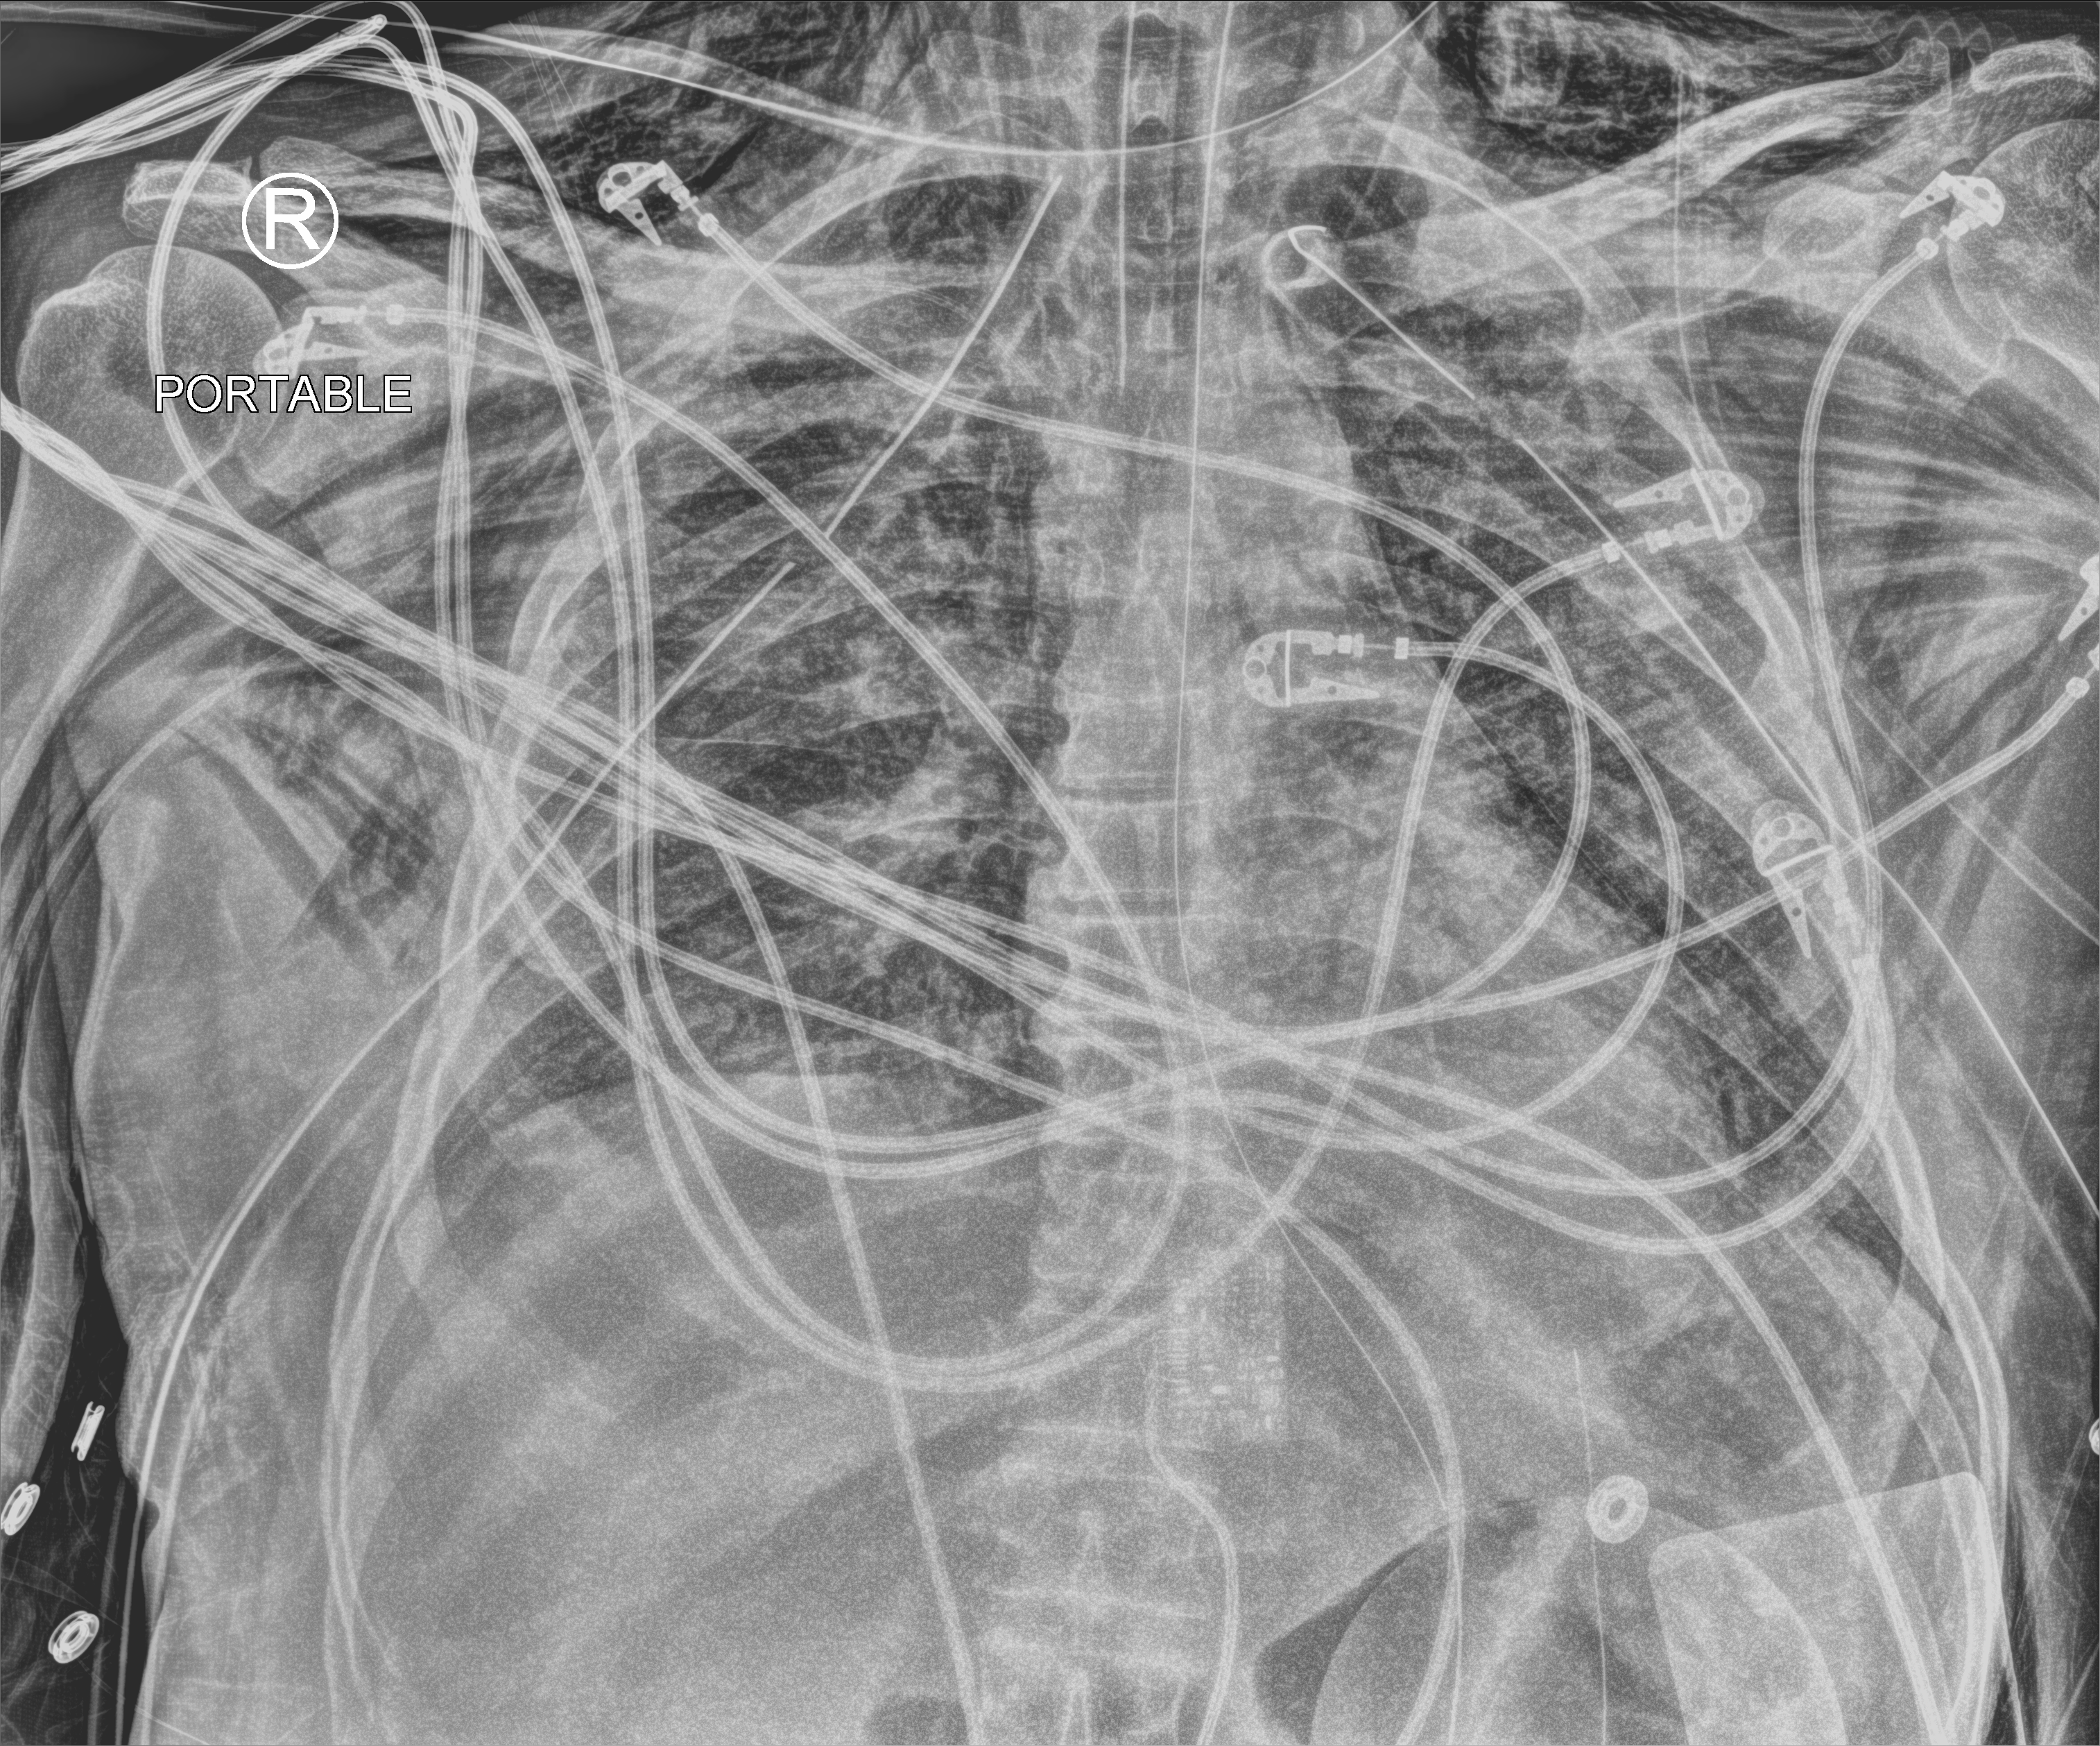
Chest X-ray (portable), anteroposterior (AP) projection. Patient hospitalised with COVID-19; male, aged 18–59 years.
Admission-level facts for this patient (not findings on this image; timing relative to this image not recorded):
- hypertension (admission record): yes